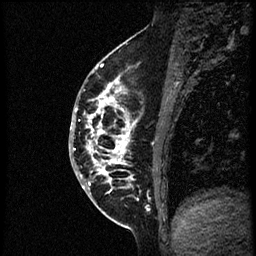
Breast MRI (dynamic contrast-enhanced), one sagittal slice. Dynamic contrast-enhanced study with each time point stored as its own series, time point 2 of 3 at this slice position (early post-contrast, ordered by acquisition time). 1.5 T. TE 4.2 ms, TR 21.3 ms. 2 mm slice thickness. 256 × 256 image matrix, field of view 200 × 200 mm. Patient: female, 41 years. Case-level facts recorded for this patient, not image findings: setting: breast cancer imaged before/during neoadjuvant chemotherapy; receptor status: HER2-positive.
Annotated regions visible in this slice (semi-automatic segmentation, software-assisted and operator-edited):
- analysis volume of interest (the breast-tissue region the enhancement analysis was run in; not a lesion): bounding box (x1, y1, x2, y2) in pixels: (70, 73, 176, 205)
- tumour enhancement mask (voxels above the 100 % enhancement threshold inside the analysis volume of interest): (74, 75, 136, 191)